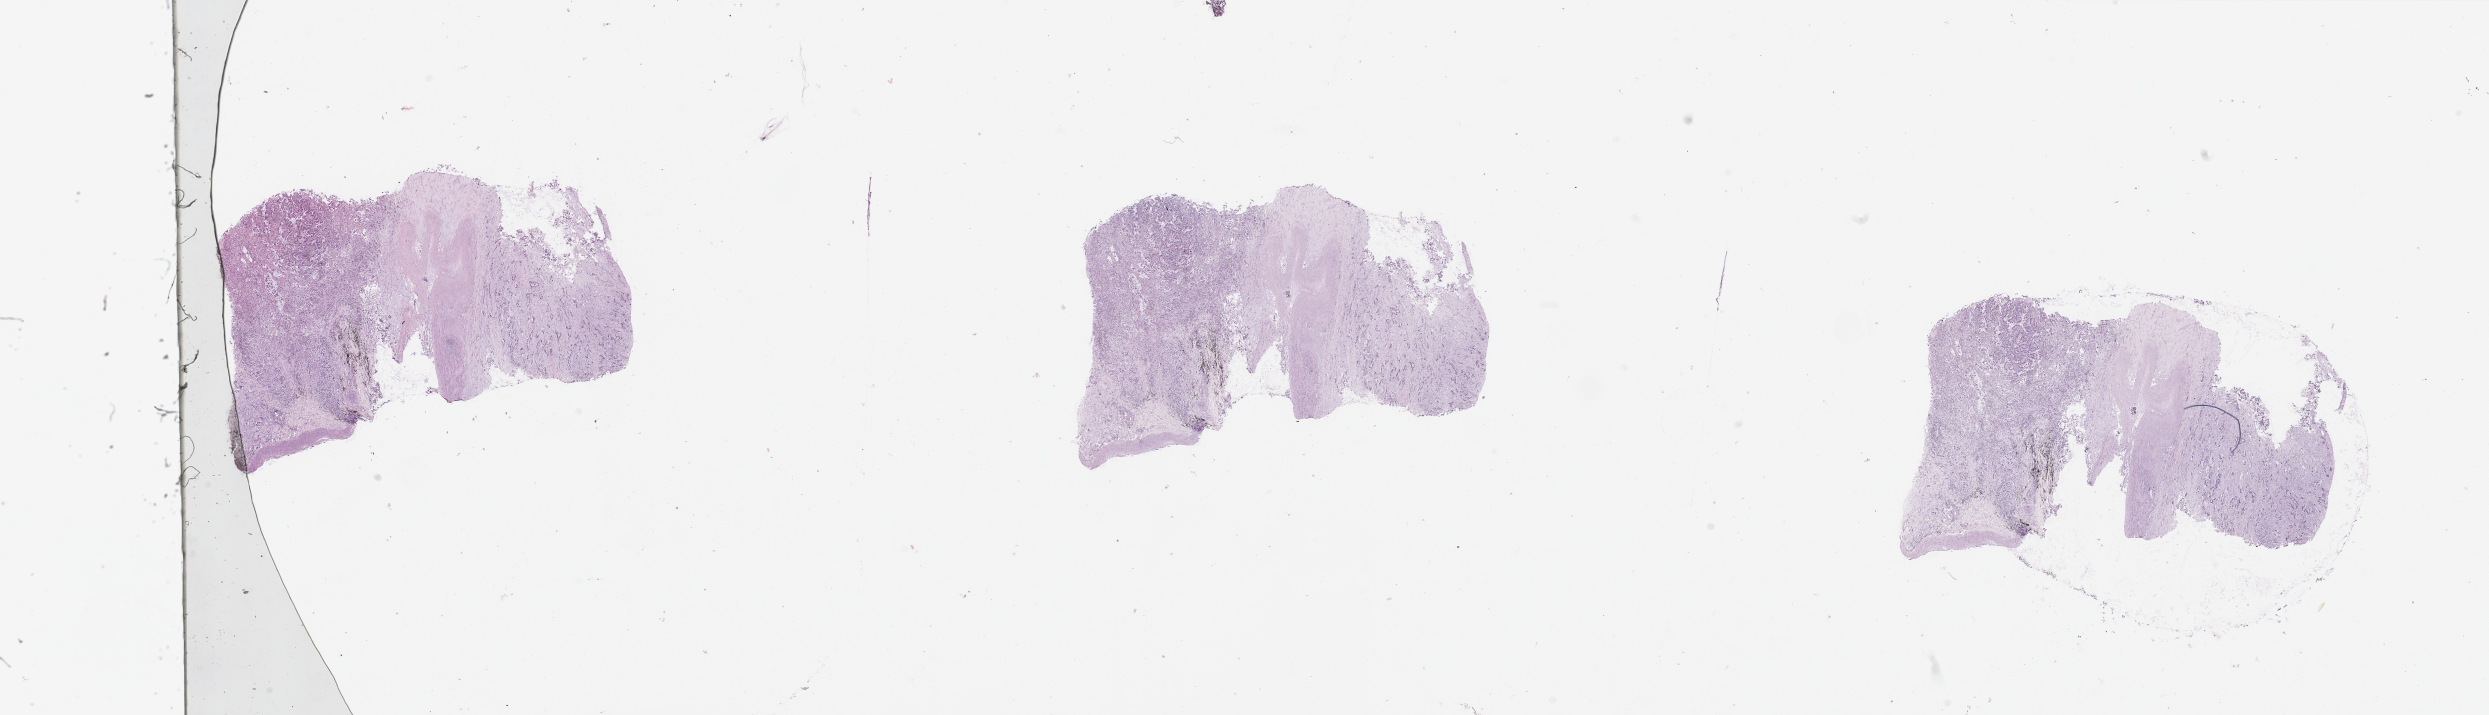
H&E-stained whole-slide image — low-resolution overview of the scanned area, about 39.4 x 11.3 mm (acquisition: 20x scan), tumour tissue sample, sampled site: lung. Male, 76 y/o. Histologic grade: G2 (moderately differentiated). Pathologist review of this section (percent, as recorded): tumour nuclei 65%, necrosis 5%.
Histologic diagnosis: Adenocarcinoma, NOS. AJCC pathologic stage: IIA.